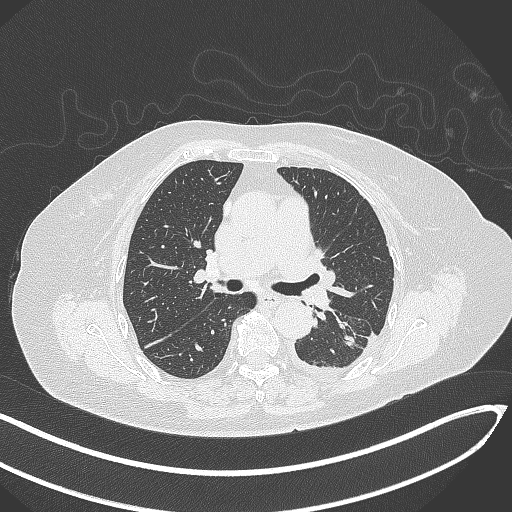
Chest CT, one axial slice; slice 189 of 270 in the series (ordered by position); 120 kVp; lung window (W 1500 / L -600 HU); 1 mm slice thickness; 512 × 512 image matrix, field of view 400 × 400 mm. Patient: female, 76 years. Case-level facts recorded for this patient, not image findings: clinical TNM (as recorded): T1c N0 M0.
Outlined on this slice (rectangle marked by the reading radiologist):
- lung tumour (recorded histology: adenocarcinoma): box from (x=335, y=330) to (x=360, y=353) px